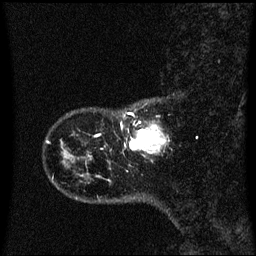
Breast MRI (dynamic contrast-enhanced), one sagittal slice; slice 8 of 60 in the series (ordered by position); dynamic contrast-enhanced series, image 2 of 3 at this slice position (ordered by acquisition); 1.5 T; TE 4.2 ms, TR 8.4 ms; 2 mm slice thickness; 256 × 256 image matrix, field of view 220 × 220 mm. Patient: female, 41 years. Case-level facts recorded for this patient, not image findings: setting: breast cancer imaged before/during neoadjuvant chemotherapy; receptor status: triple-negative.
Annotated regions visible in this slice (semi-automatically segmented with operator editing):
- analysis volume of interest (the breast-tissue region the enhancement analysis was run in; not a lesion): bounding box [x1, y1, x2, y2] px = [124, 116, 162, 153]
- tumour enhancement mask (voxels above the 70 % enhancement threshold inside the analysis volume of interest): [131, 130, 162, 149]